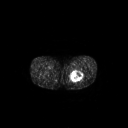
FDG PET of an extremity soft-tissue mass (from a PET/CT study), one axial slice. 3.27 mm slice thickness. 128 × 128 image matrix. Patient: male, 44 years. From the clinical record (not read from this slice): histological type: undifferentiated pleomorphic liposarcoma; grade: high; site of the primary tumour: left thigh.
Outlined on this slice (expert contour drawn on MRI and transferred to this co-registered scan by the dataset authors):
- gross tumour volume including surrounding oedema: bounding box [x1, y1, x2, y2] px = [69, 71, 83, 82]
- gross tumour volume (mass): [70, 71, 82, 82]